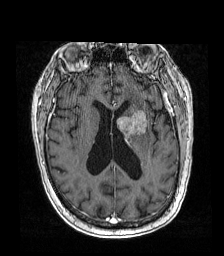
Brain MRI from a brain-tumour surgery series, one axial slice; position 75 of 192 along the scan axis; T1-weighted post-contrast; 1 mm slice thickness; 224 × 256 image matrix, field of view 219 × 250 mm. Case-level facts recorded for this patient, not image findings: histopathology: Metastatic carcinoma from lung primary; tumour location: Left Frontal Caudate.
Outlined on this slice (expert manual segmentation):
- tumour: bounding box (x1, y1, x2, y2) in pixels: (117, 110, 148, 145)